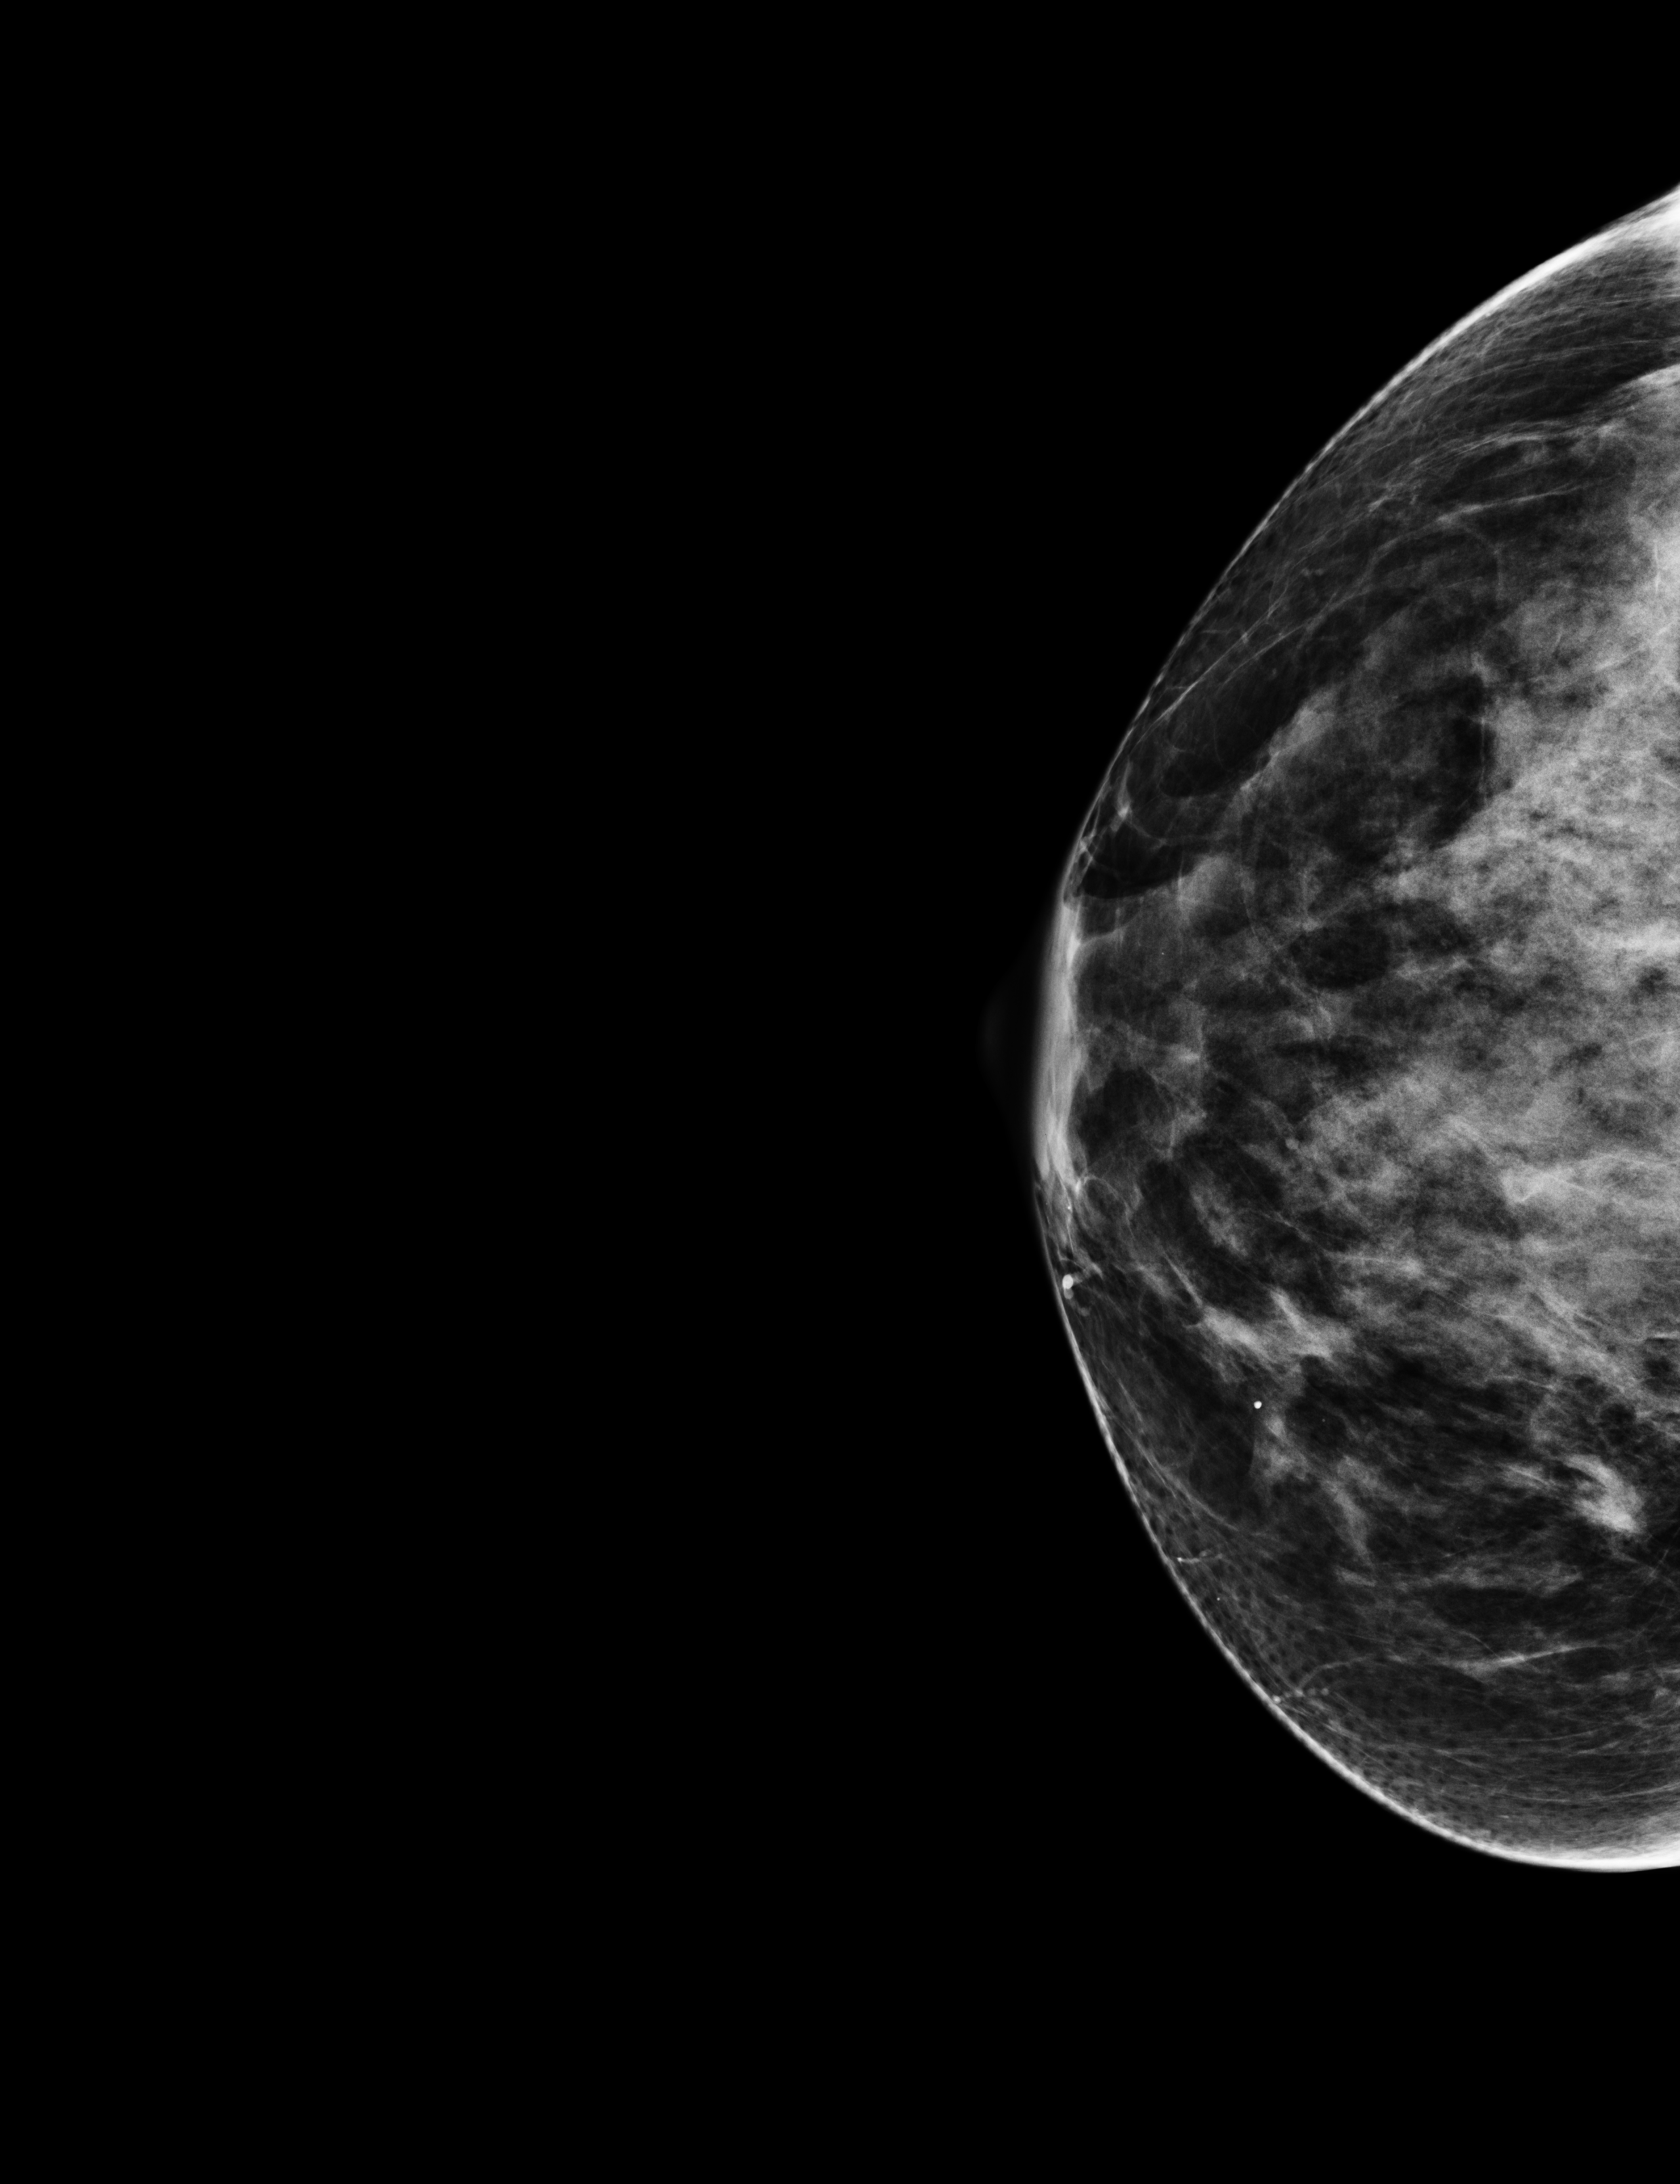
Digital mammogram (FFDM); right breast; CC view; annual screening mammography examination; compressed breast thickness 61 mm. Patient: female, 64 years.
- breast density at the screening exam (both breasts): extremely dense (BI-RADS density category d)
- final BI-RADS category for the screening round (tomosynthesis exam, both breasts): category 1
- recall: no recall after this screen